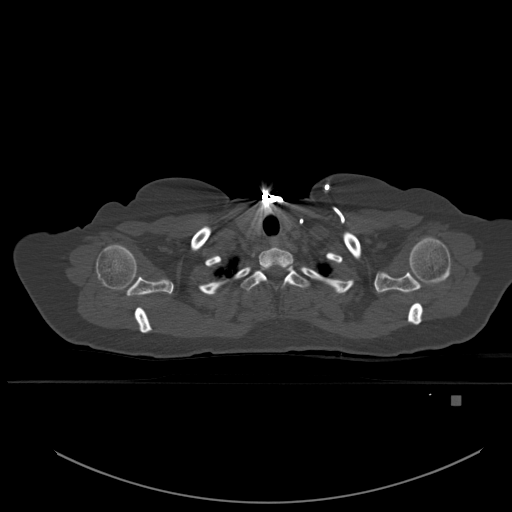
CT including the spine, one axial slice. Slice 422 of 651 in the series (ordered by position). Bone window (W 1800 / L 400 HU). 1.5 mm slice thickness. 512 × 512 image matrix, field of view 443 × 443 mm. Female patient, age 49 years. From the clinical record (not read from this slice): primary cancer: breast; vertebrae with lytic lesions (as recorded): L3, T12, L4.
Structures marked on this image (semi-automatically segmented with operator editing):
- T1 vertebra: bounding box [x1, y1, x2, y2] px = [241, 266, 308, 291]